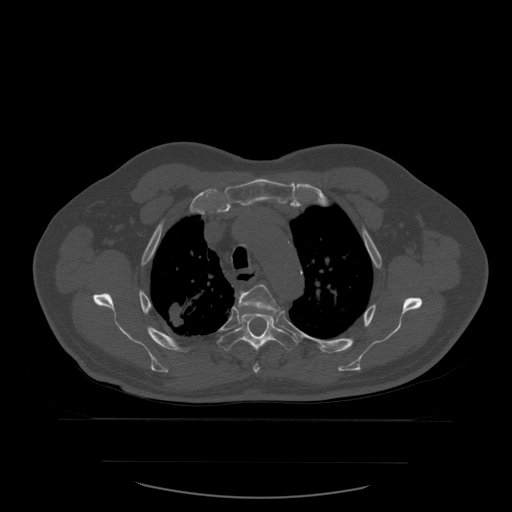
CT including the spine, one axial slice; slice 431 of 590 in the series (ordered by position); bone window (W 1800 / L 400 HU); 1.25 mm slice thickness; 512 × 512 image matrix. Patient age 71 years. Case-level facts recorded for this patient, not image findings: primary cancer: lung; vertebrae with lytic lesions (as recorded): T1, T2, L5, S1.
Annotated regions visible in this slice (semi-automatically segmented with operator editing):
- T4 vertebra: box from (x=235, y=285) to (x=281, y=373) px
- T5 vertebra: (x=217, y=312)–(x=299, y=352)